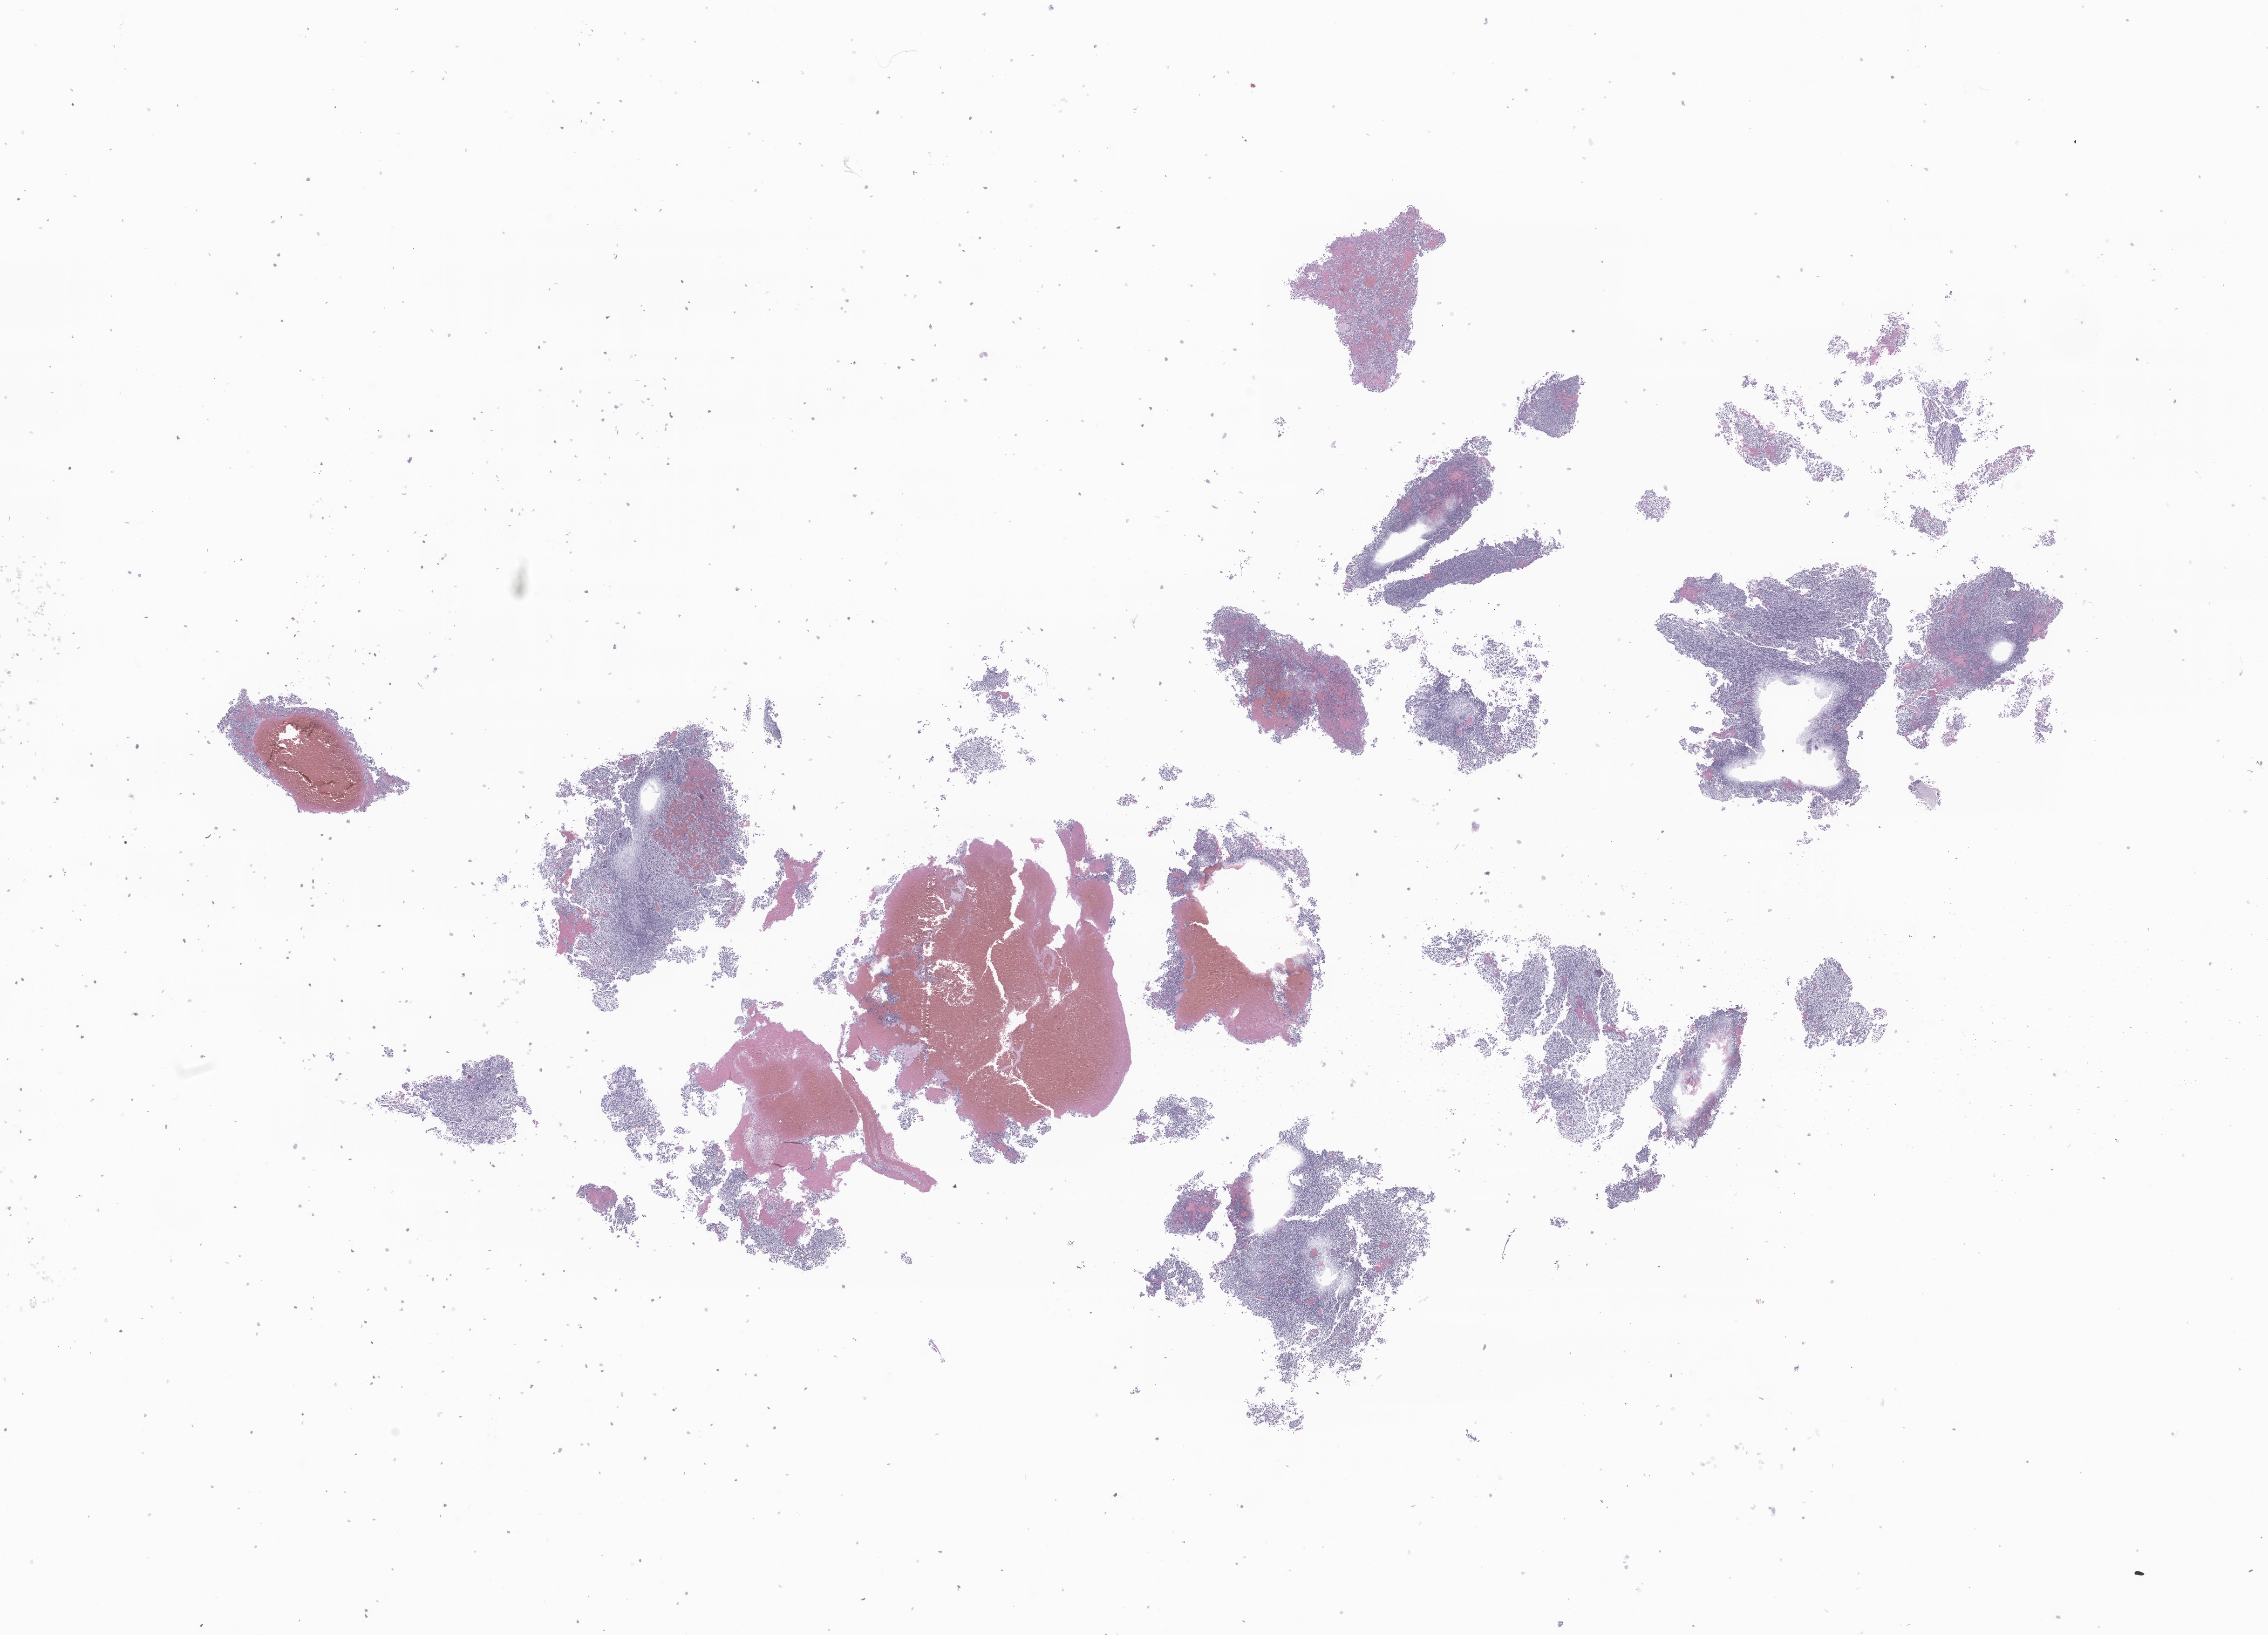
Whole-slide image, haematoxylin and eosin stain of tumor tissue from the cerebellum, shown as a low-resolution overview of the whole scanned area (about 20.5 x 14.8 mm), formalin-fixed, paraffin-embedded (FFPE) tissue. Male patient, age 226 months (18 years 10 months).
Diagnosis: Medulloblastoma, NOS.